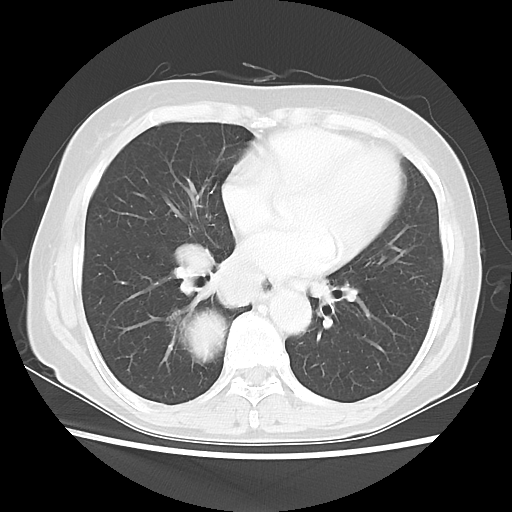
Chest CT, one axial slice. Slice 23 of 56 in the series (ordered by position). Reconstruction kernel LUNG. Lung window (W 1500 / L -600 HU). 5 mm slice thickness. 512 × 512 image matrix, field of view 332 × 332 mm. Patient: female, 66 years. From the clinical record (not read from this slice): clinical TNM (as recorded): T2 N3 M0; histopathological grade: G3.
Annotated regions visible in this slice (bounding box drawn by a radiologist):
- lung tumour (recorded histology: small cell carcinoma): bounding box (x1, y1, x2, y2) in pixels: (173, 300, 228, 371)